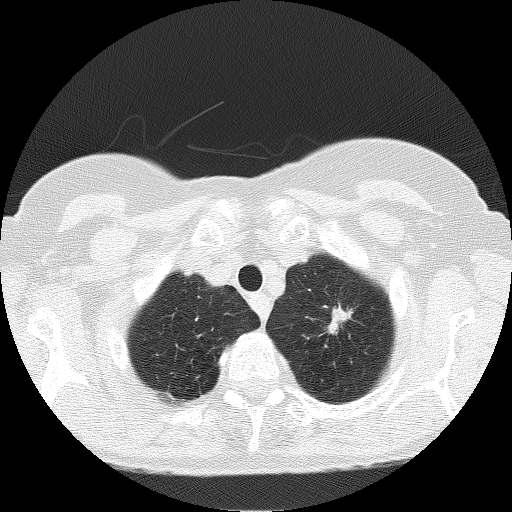
Low-dose screening chest CT, one axial slice; slice 150 of 166 in the series (ordered by position); reconstruction kernel FC51; lung window (W 1500 / L -600 HU); 2 mm slice thickness; 512 × 512 image matrix, field of view 303 × 303 mm.
Structures marked on this image (expert manual segmentation):
- lesion 3 (nodule, upper lobe of left lung): box from (x=327, y=306) to (x=351, y=333) px